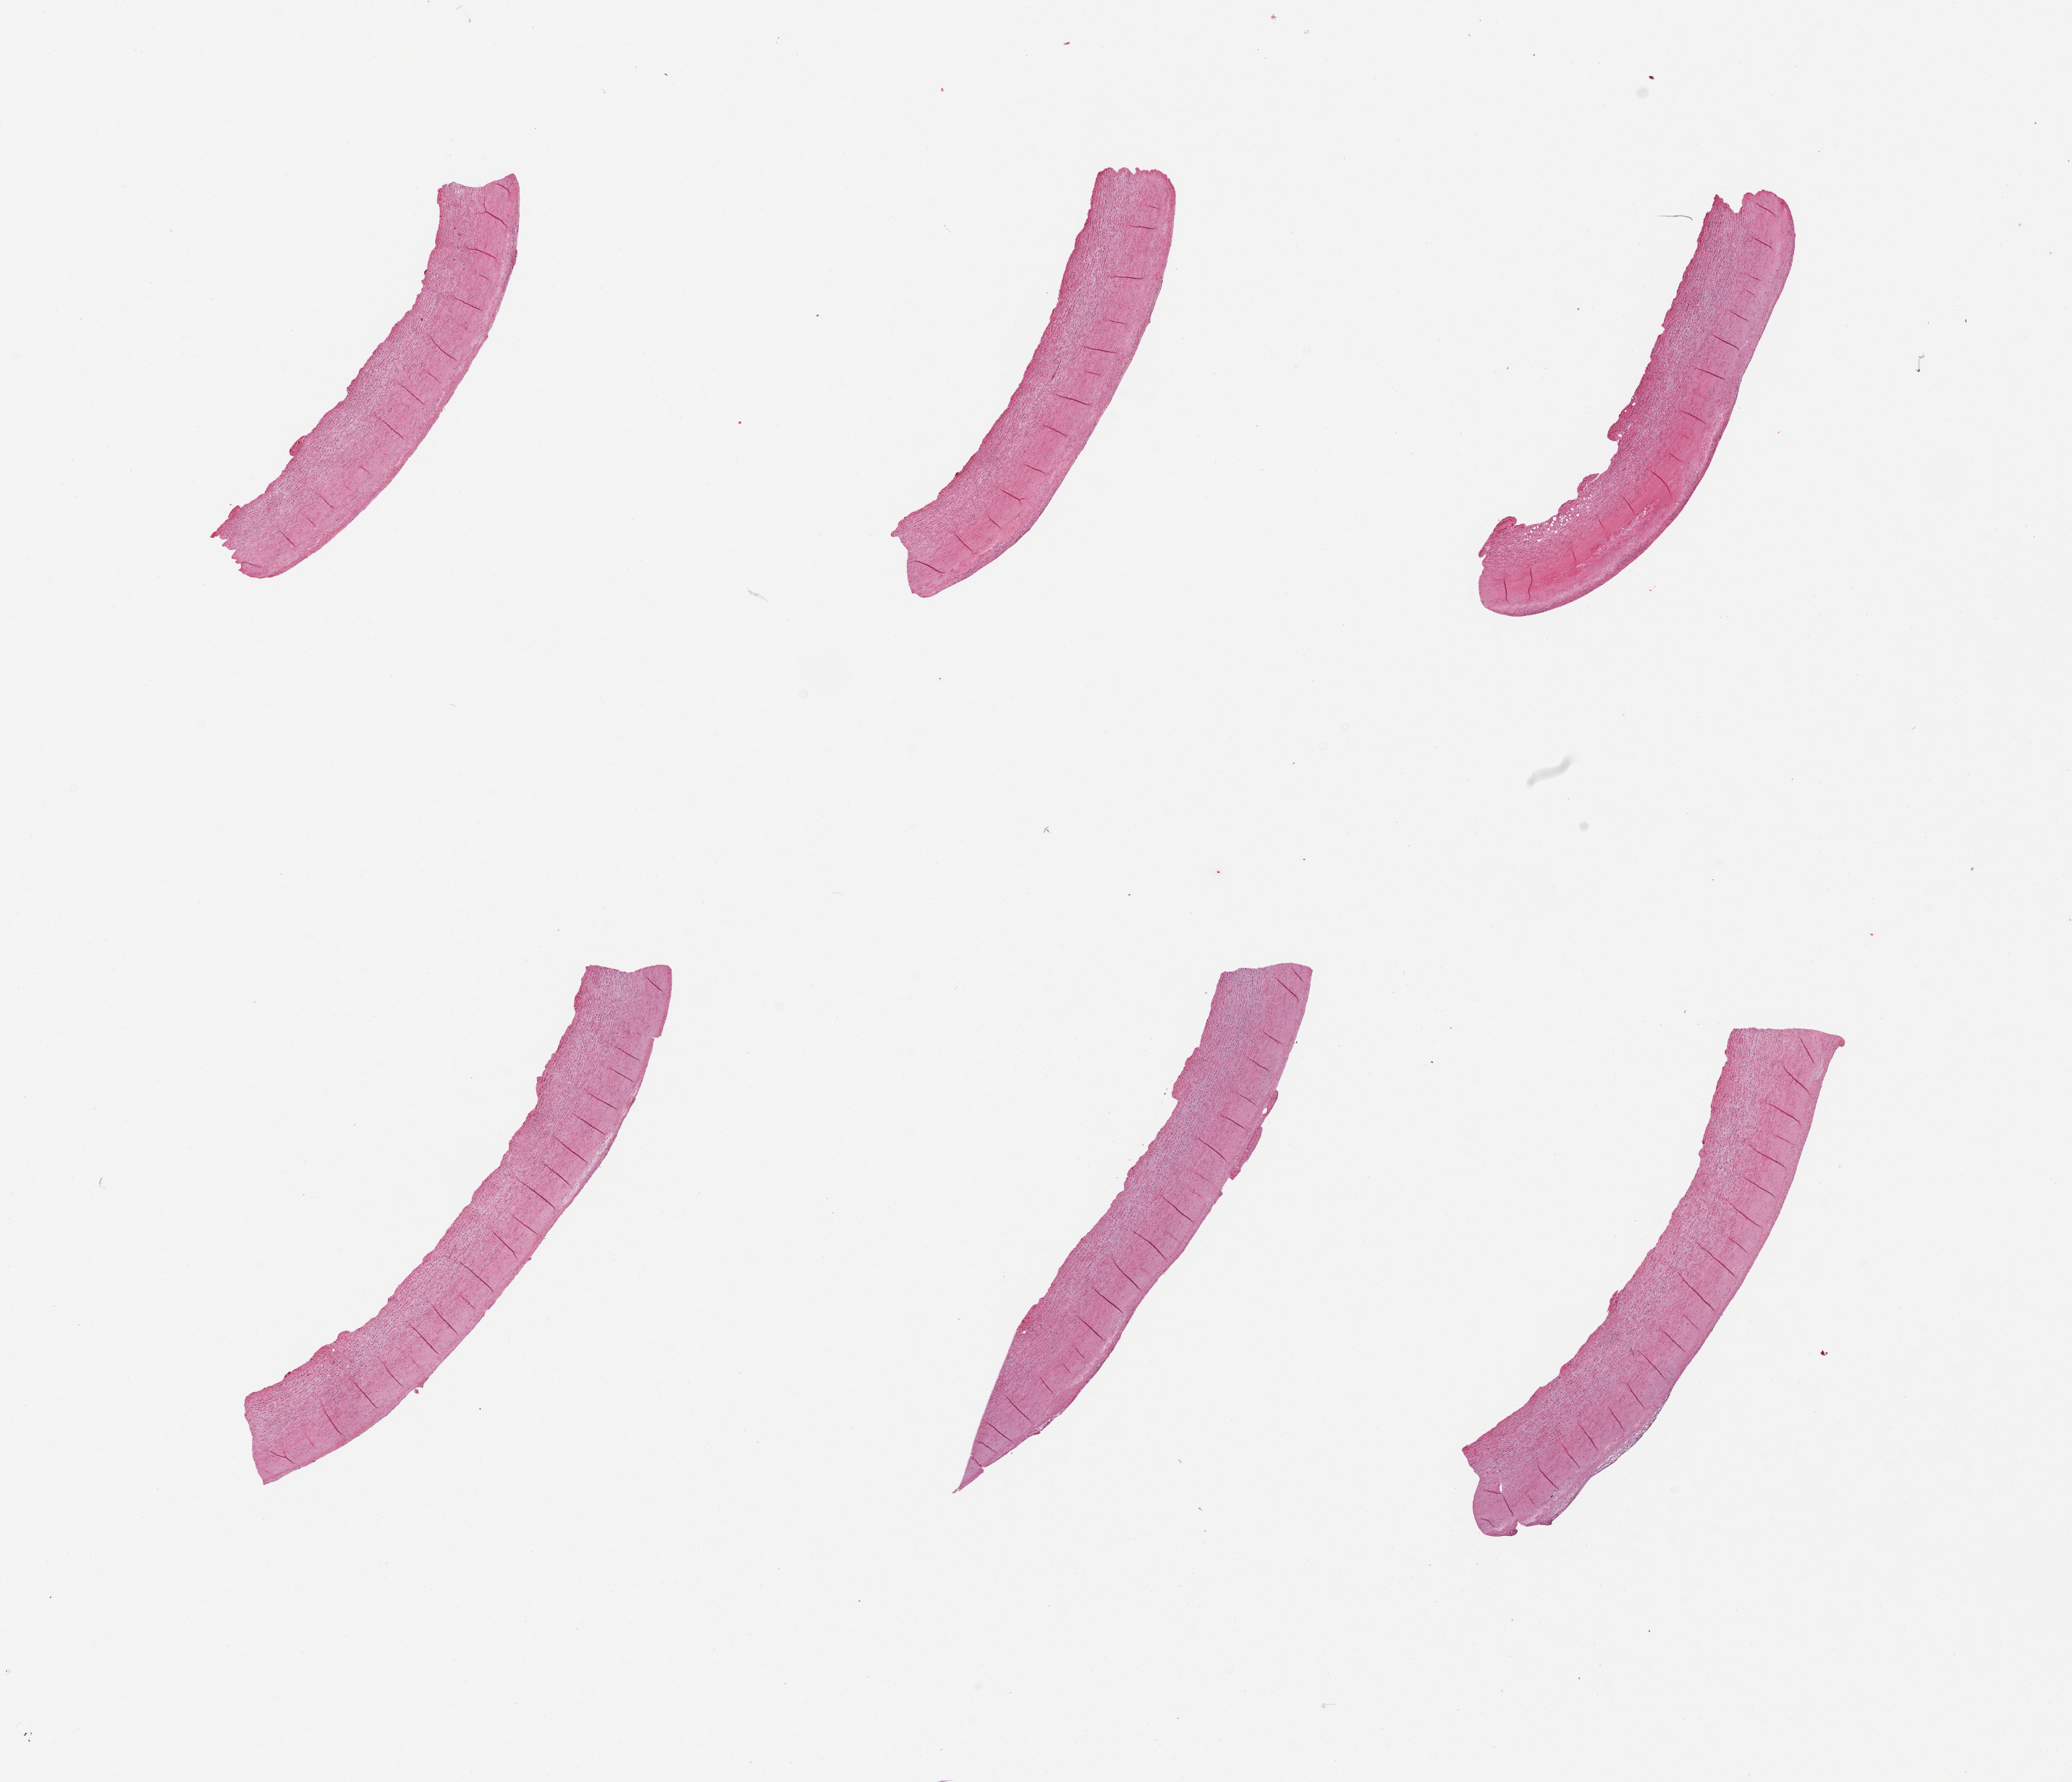
Whole-slide image, H&E stain — shown as a low-resolution overview of the whole scanned area (about 22.6 x 19.5 mm, from a 20x scan), PAXgene-fixed, paraffin-embedded tissue, section of aorta (target tissue), tissue donor sample. Donor sex: male.
Reviewer comment on this tissue sample: 6 pieces, mild atherosclerosis.